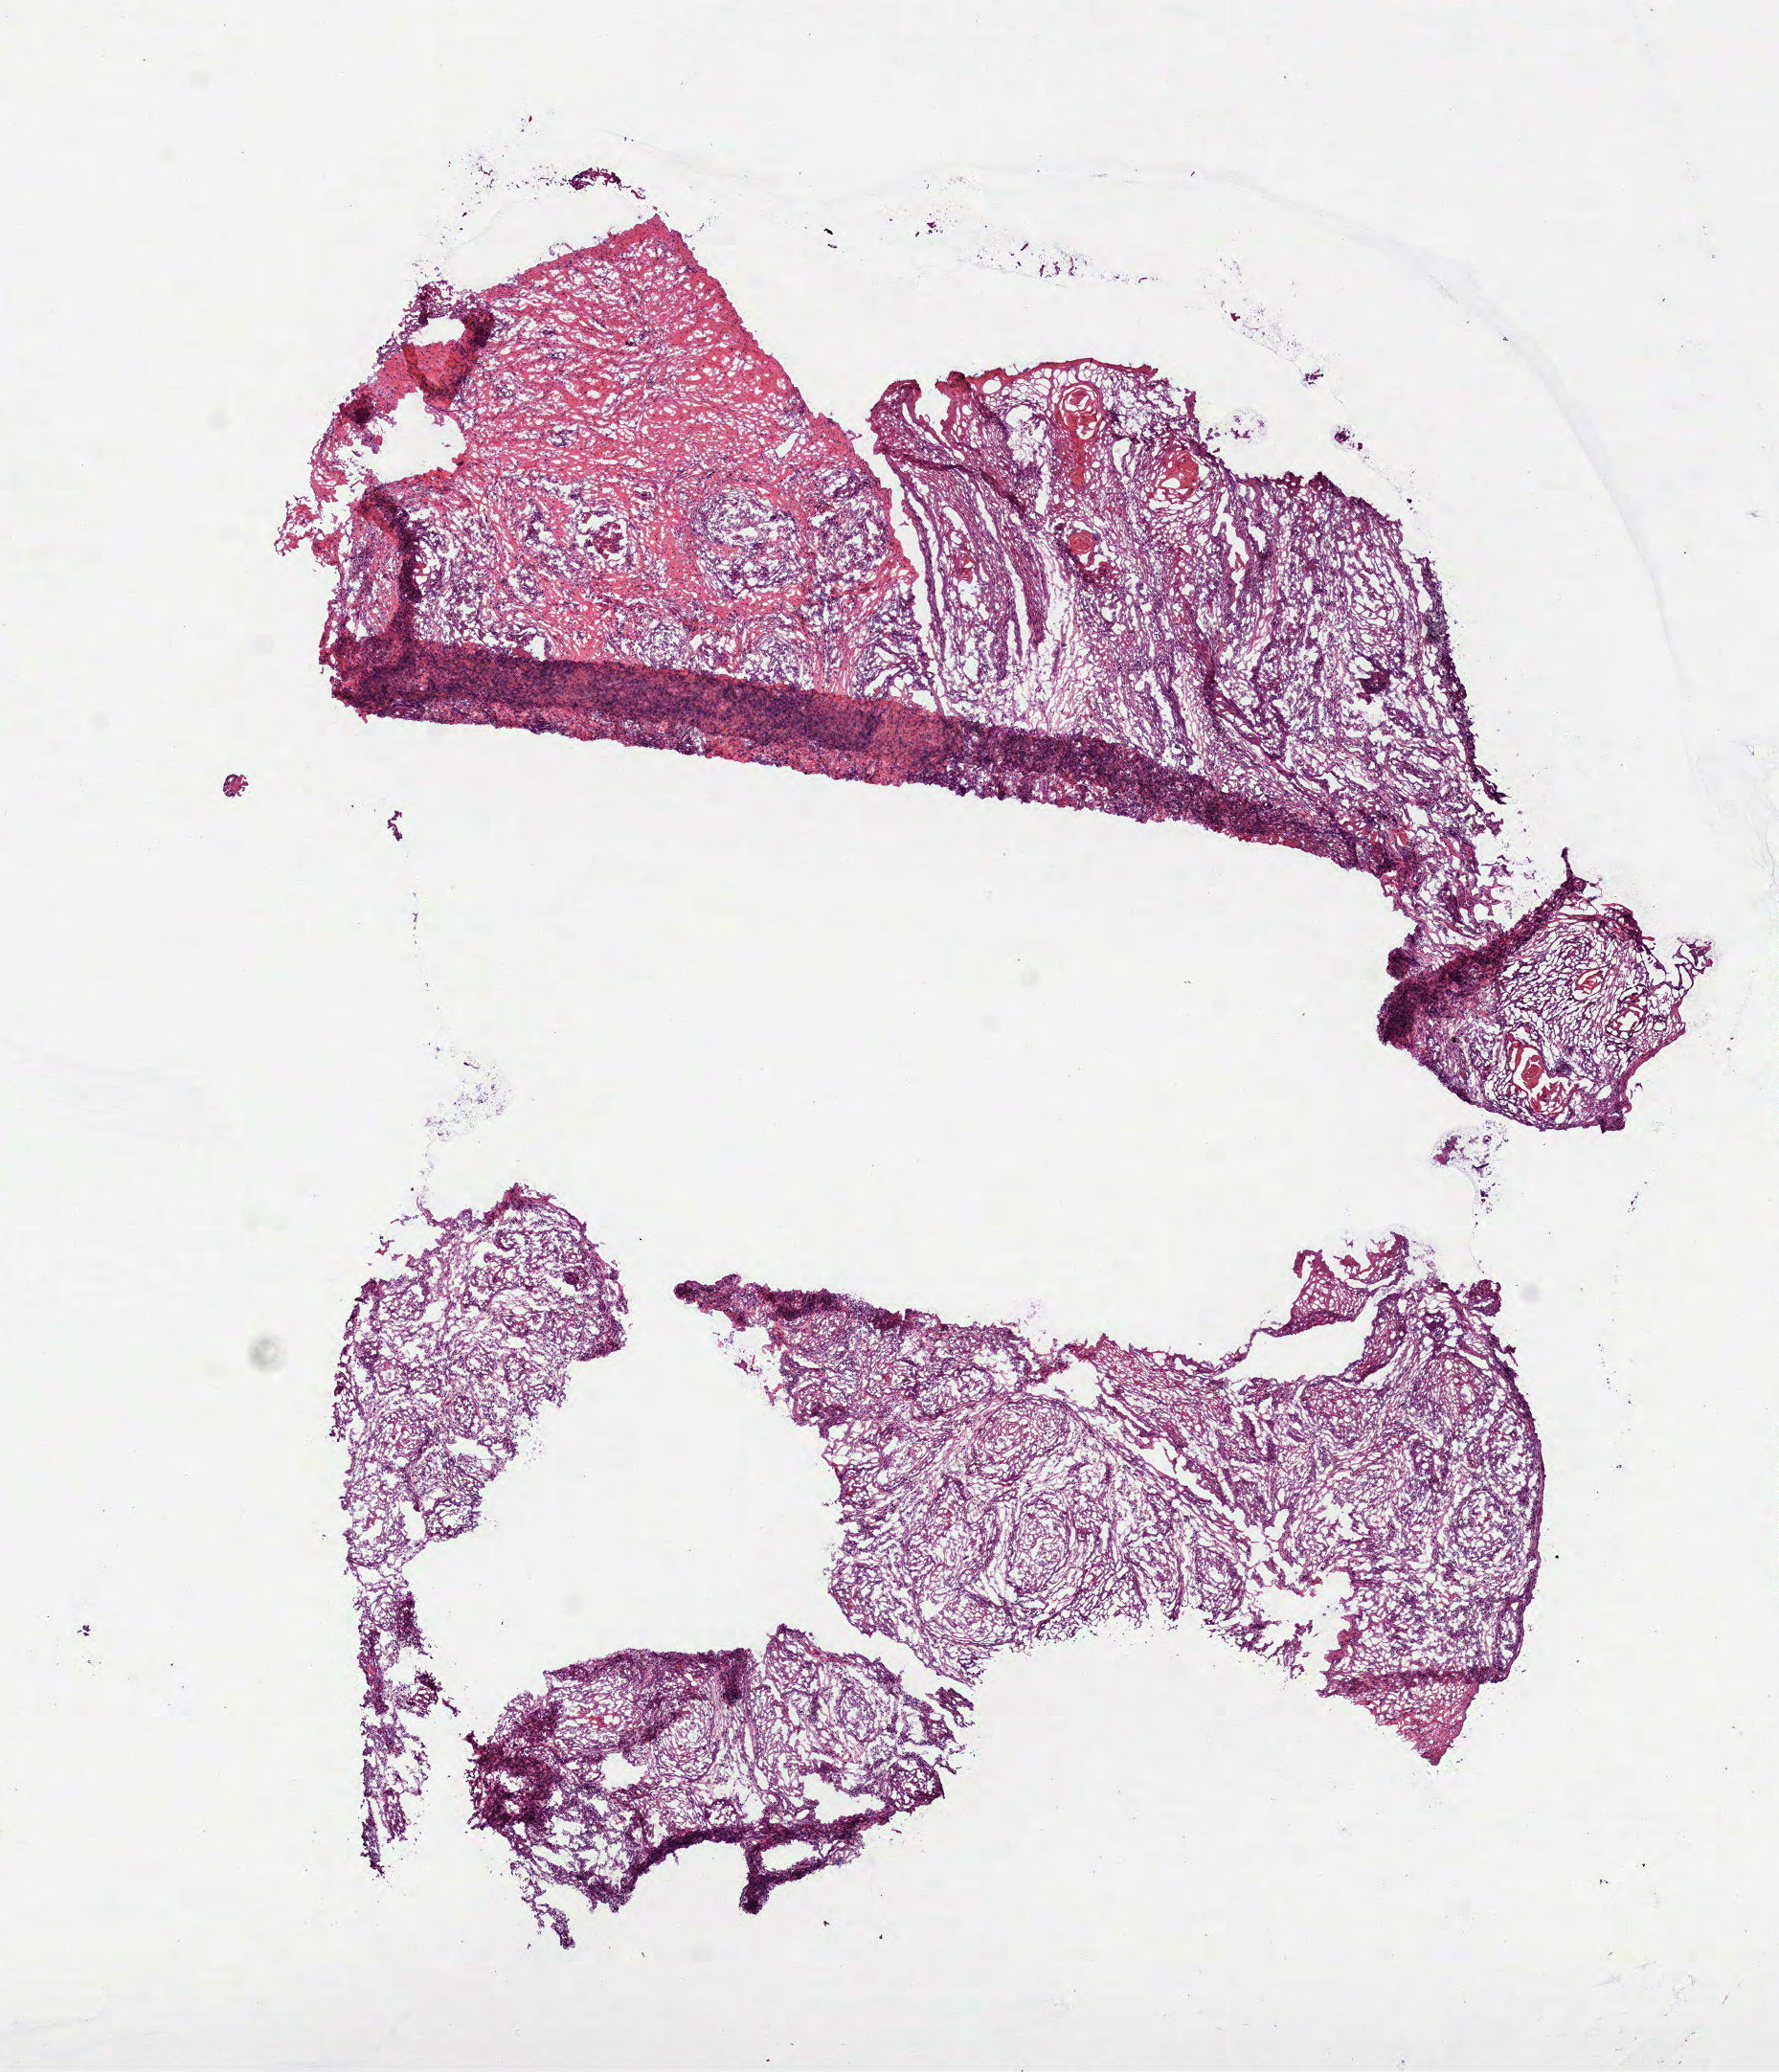
Hematoxylin and eosin (H&E) stained whole-slide image, low-resolution overview of the scanned area, about 7.5 x 8.7 mm (from a 40x scan), frozen section from the top of the tissue portion, sample: primary tumour, head and neck. Patient: male, age at initial diagnosis 87 years.
Pathologic diagnosis: Squamous cell carcinoma, NOS (overlapping lesion of lip, oral cavity and pharynx).